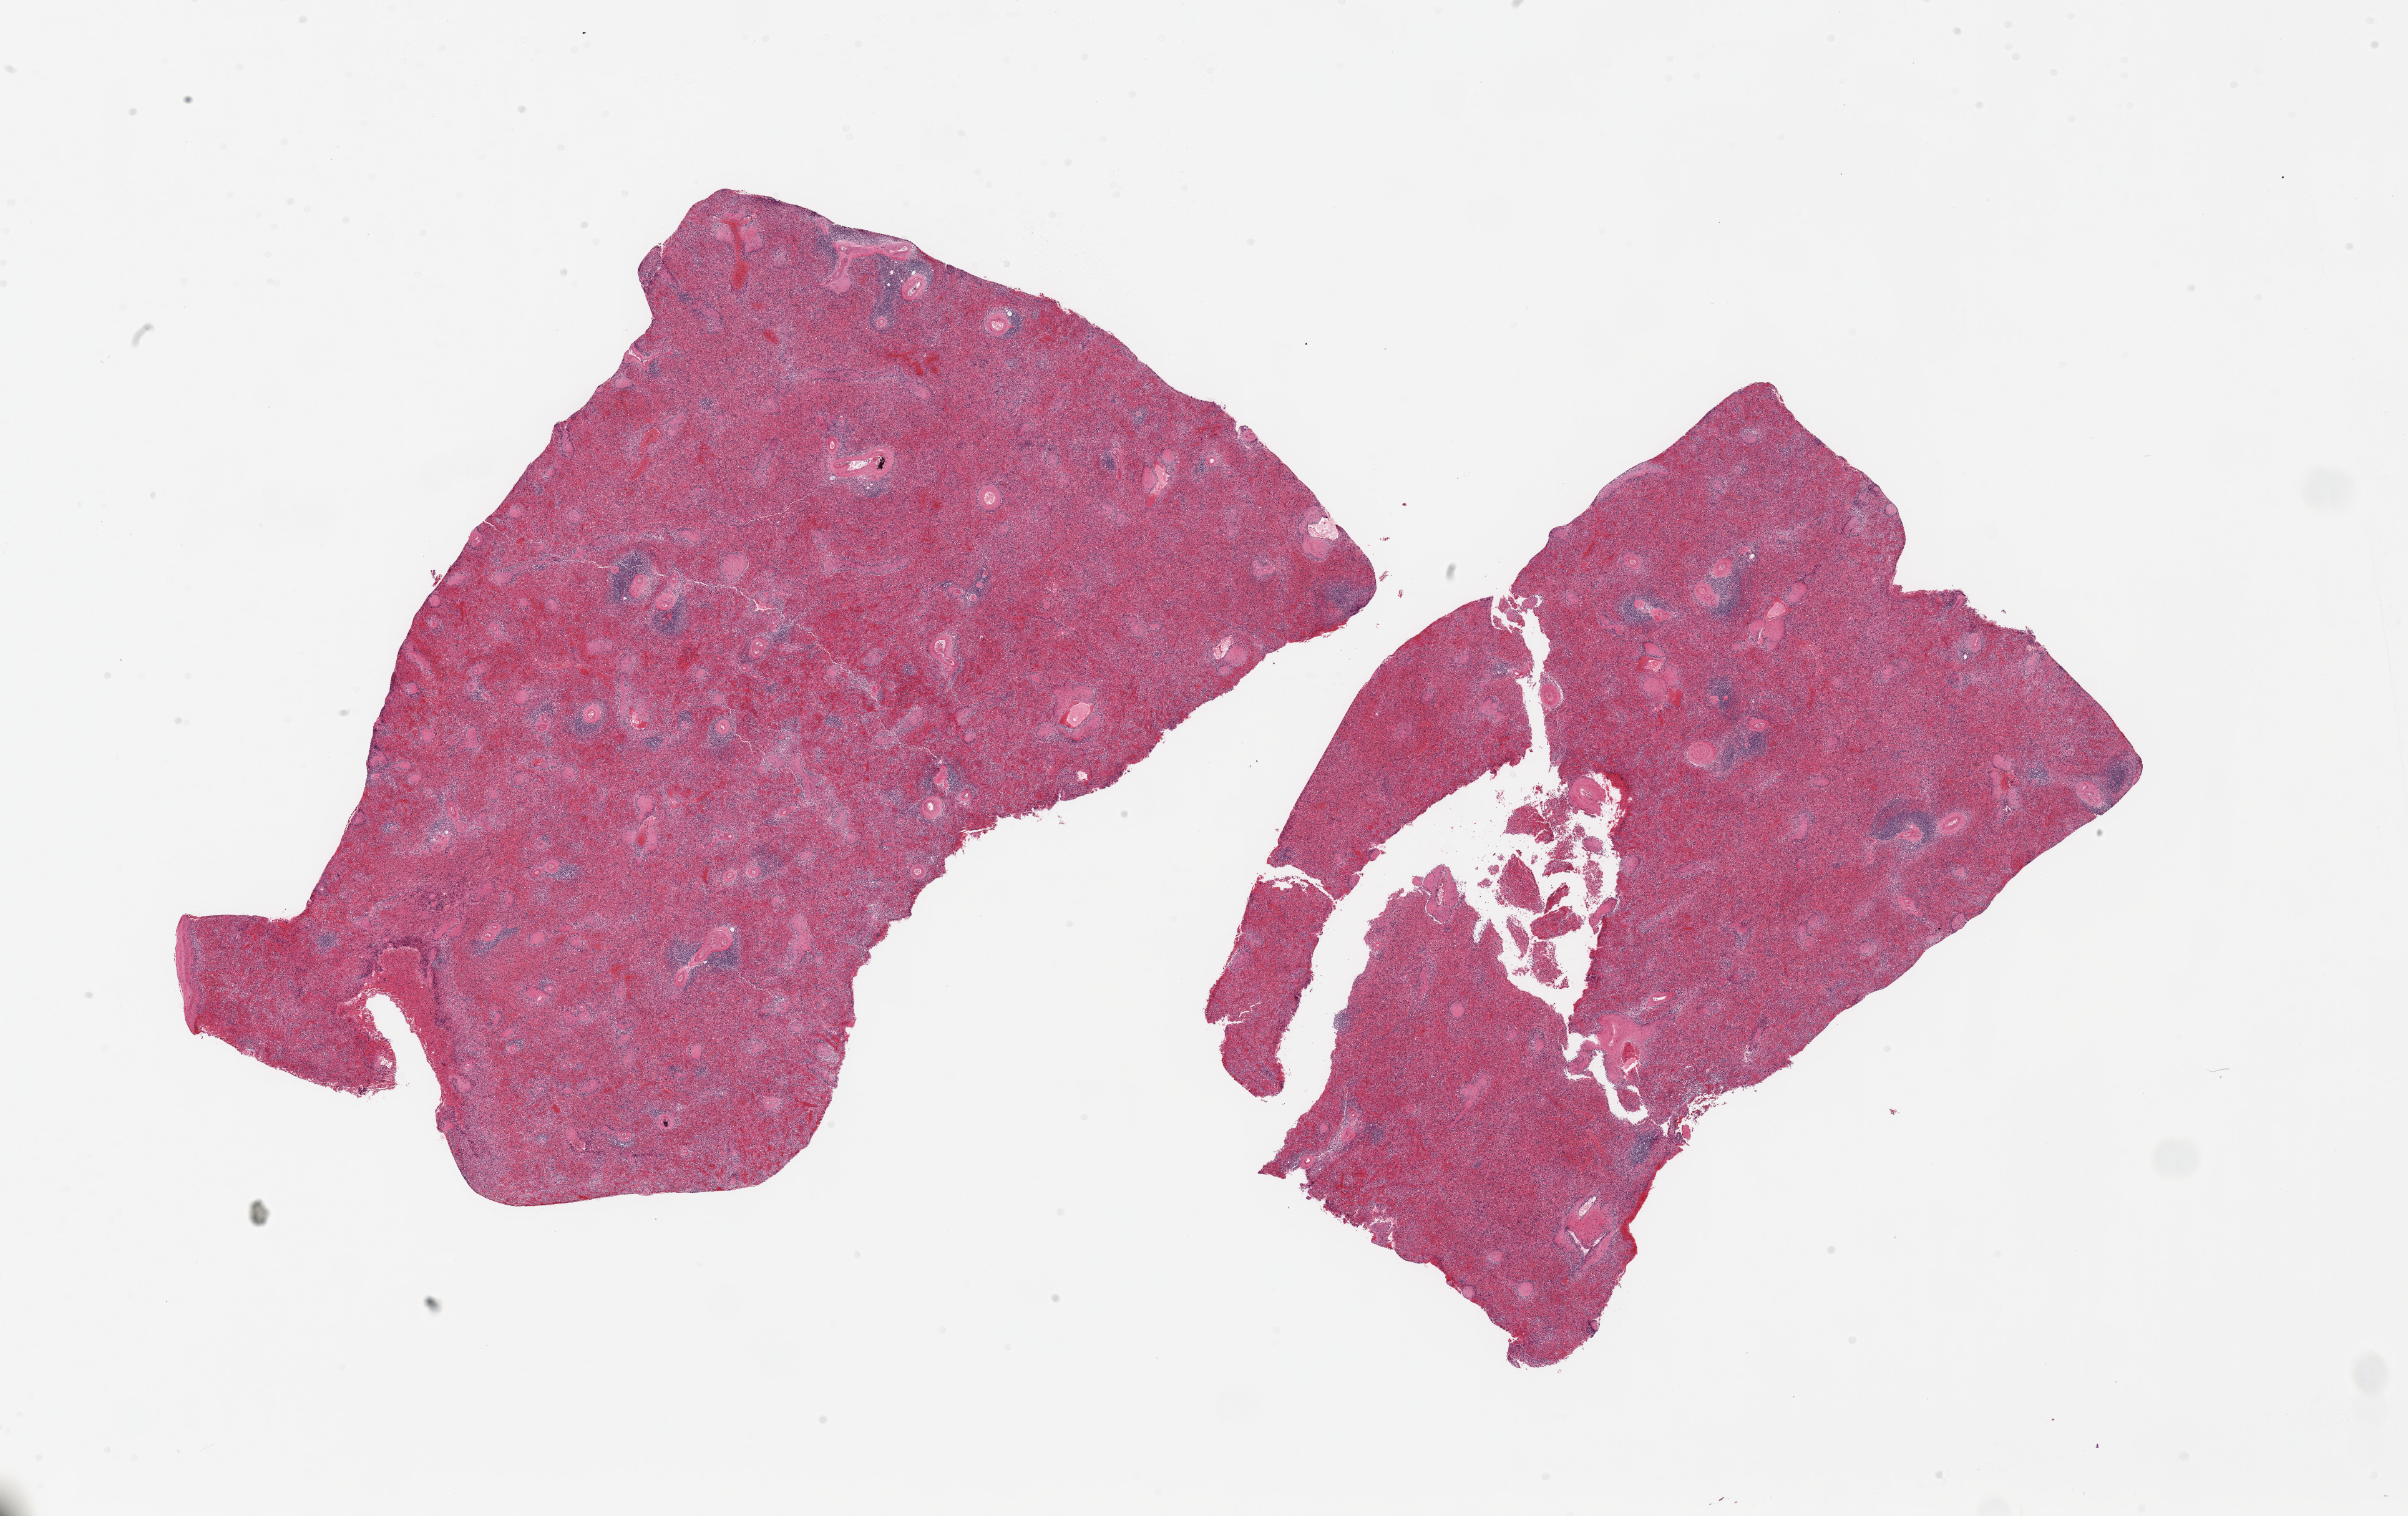
Digitized hematoxylin and eosin (H&E)-stained section, whole scanned area (about 30.5 x 19.2 mm, from a 20x scan) shown as a low-resolution overview; PAXgene-fixed, paraffin-embedded tissue; target tissue: spleen; donor tissue sample. Donor sex: male.
Reviewer comment on this tissue sample: 2 pieces; moderately congested.